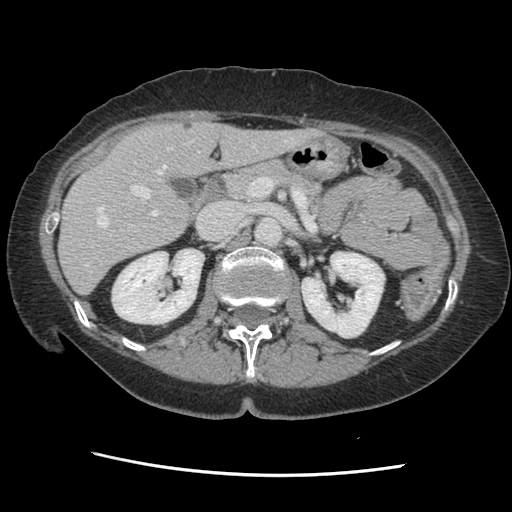
Contrast-enhanced abdominal CT, one axial slice; position 76 of 141 along the scan axis; soft-tissue window (W 400 / L 40 HU); 2.5 mm slice thickness; 512 × 512 image matrix, field of view 330 × 330 mm. Female patient, age 61 years. From the clinical record (not read from this slice): diagnosis: colorectal cancer liver metastases, imaged before liver resection; multiple liver metastases: no; largest metastasis: 2.4 cm; disease in both lobes: no.
Outlined on this slice (manually delineated by an expert):
- hepatic veins: bounding box [x1, y1, x2, y2] px = [86, 142, 256, 266]
- liver: [60, 123, 312, 293]
- planned liver remnant (the part of the liver to remain after resection): [60, 123, 312, 293]
- portal vein (with intrahepatic branches): [130, 185, 158, 216]
- liver metastasis: [183, 121, 193, 131]